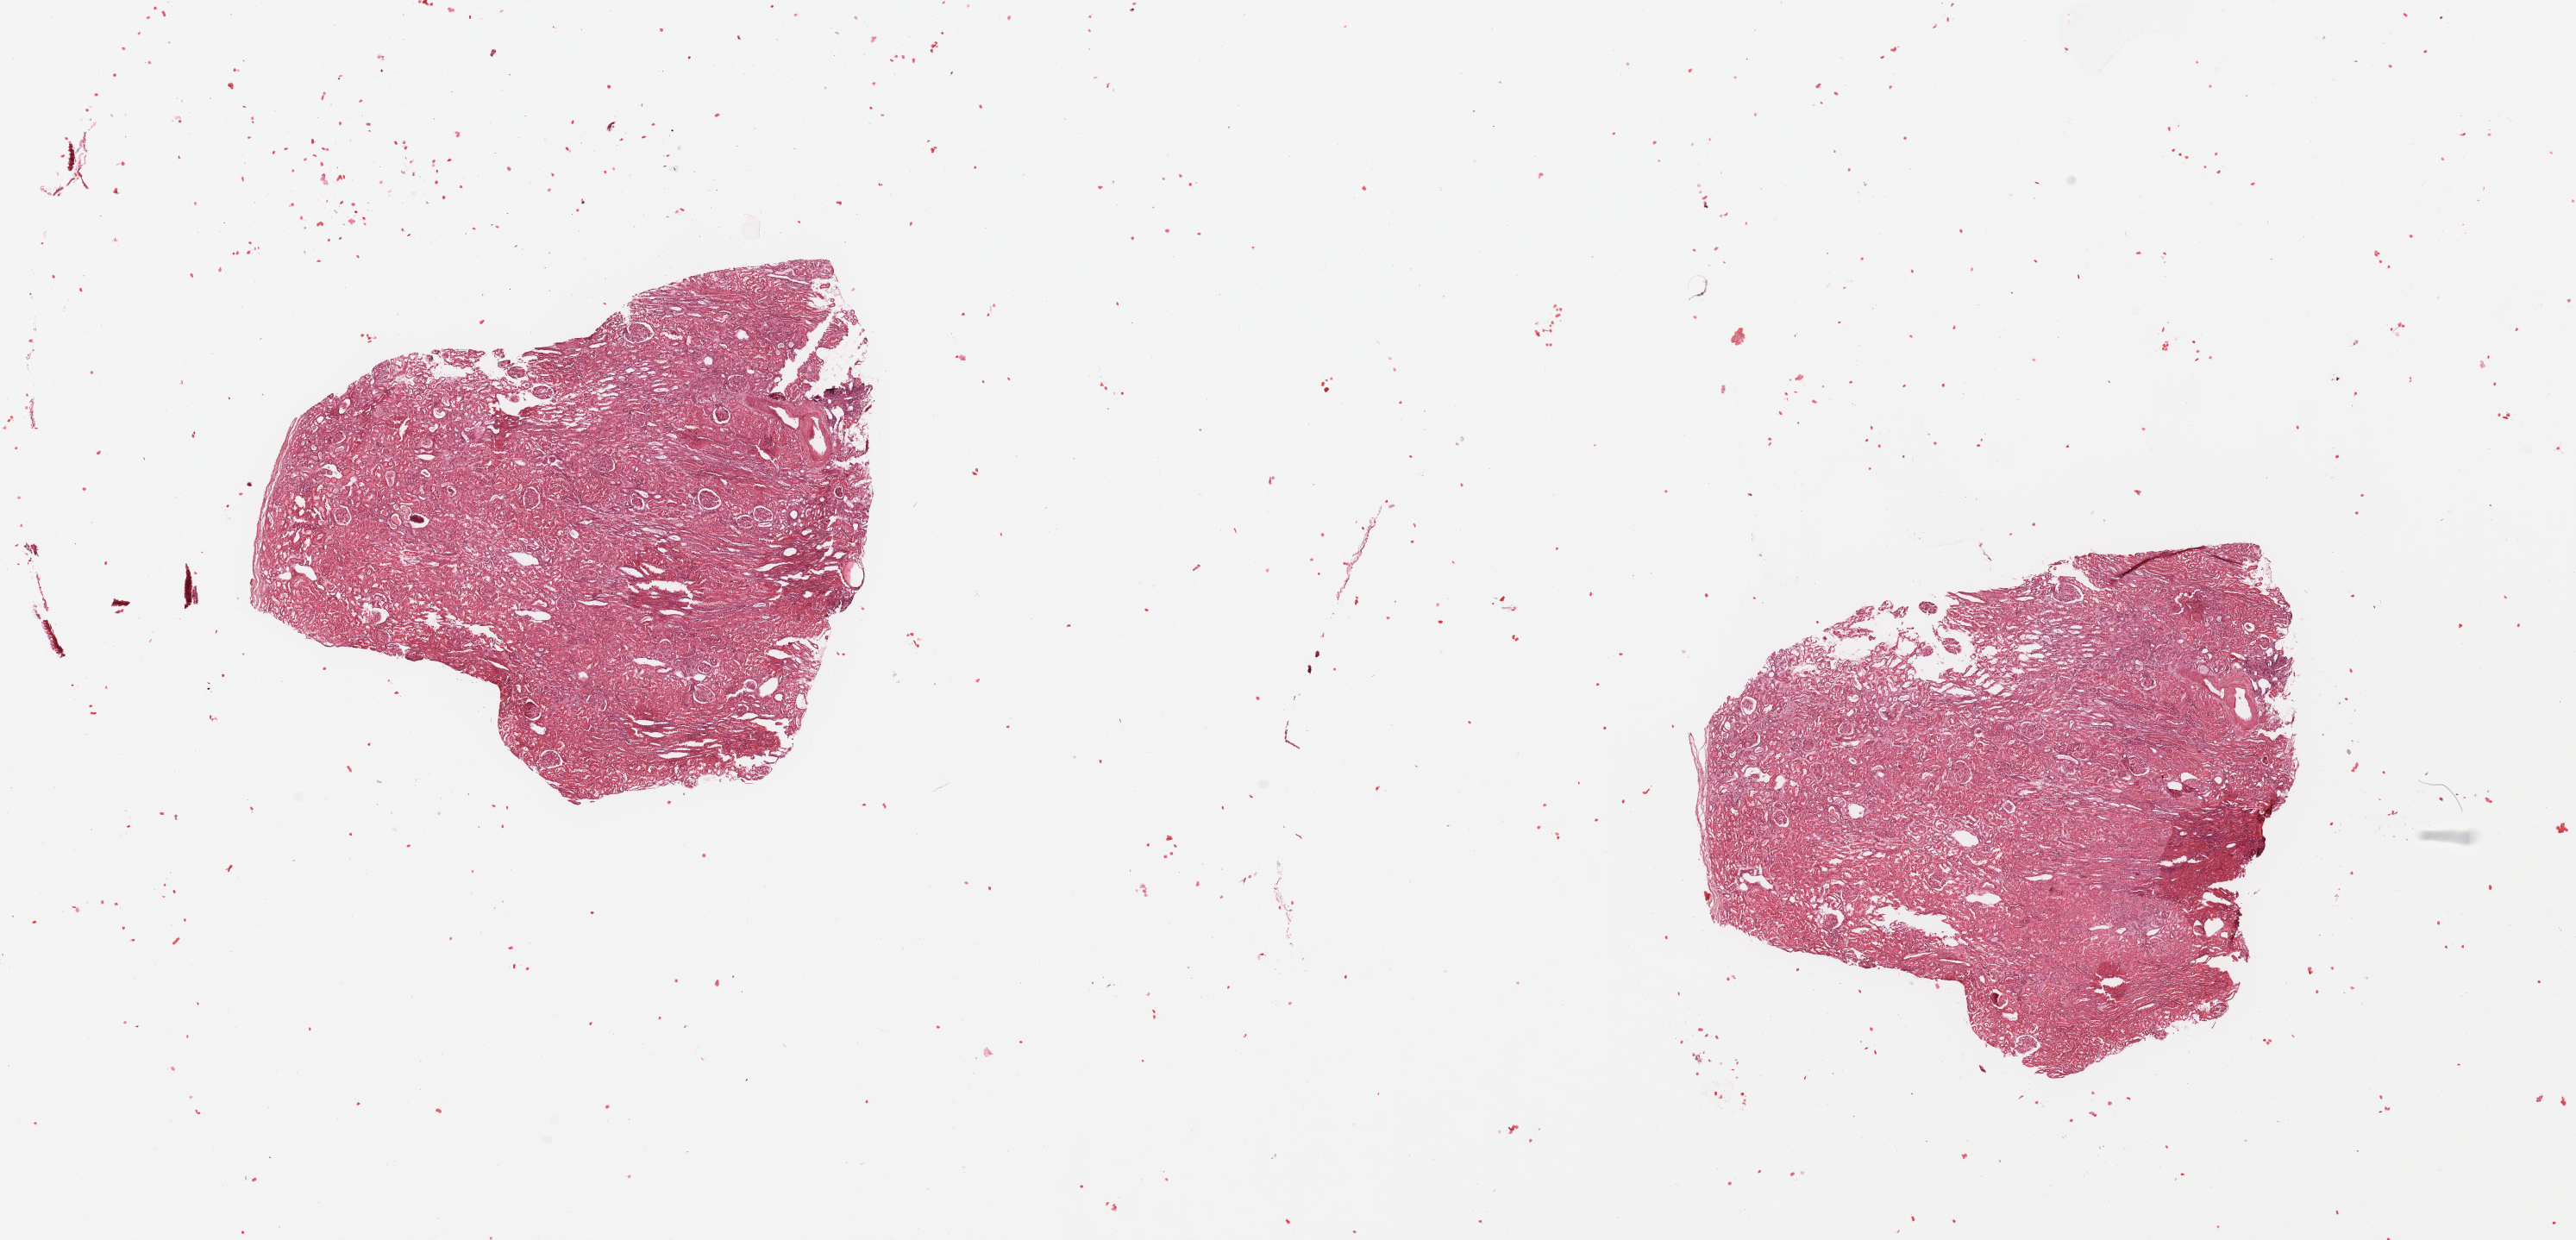
Whole-slide histology image, Hematoxylin and eosin (H&E) stained, whole scanned area (about 23.6 x 11.4 mm, acquisition: 20x scan) shown as a low-resolution overview. Normal (non-tumour) tissue sample, sampled site: kidney. 52-year-old male patient.
- this section: normal (non-tumour) tissue from the same patient
- patient diagnosis: Renal cell carcinoma, NOS